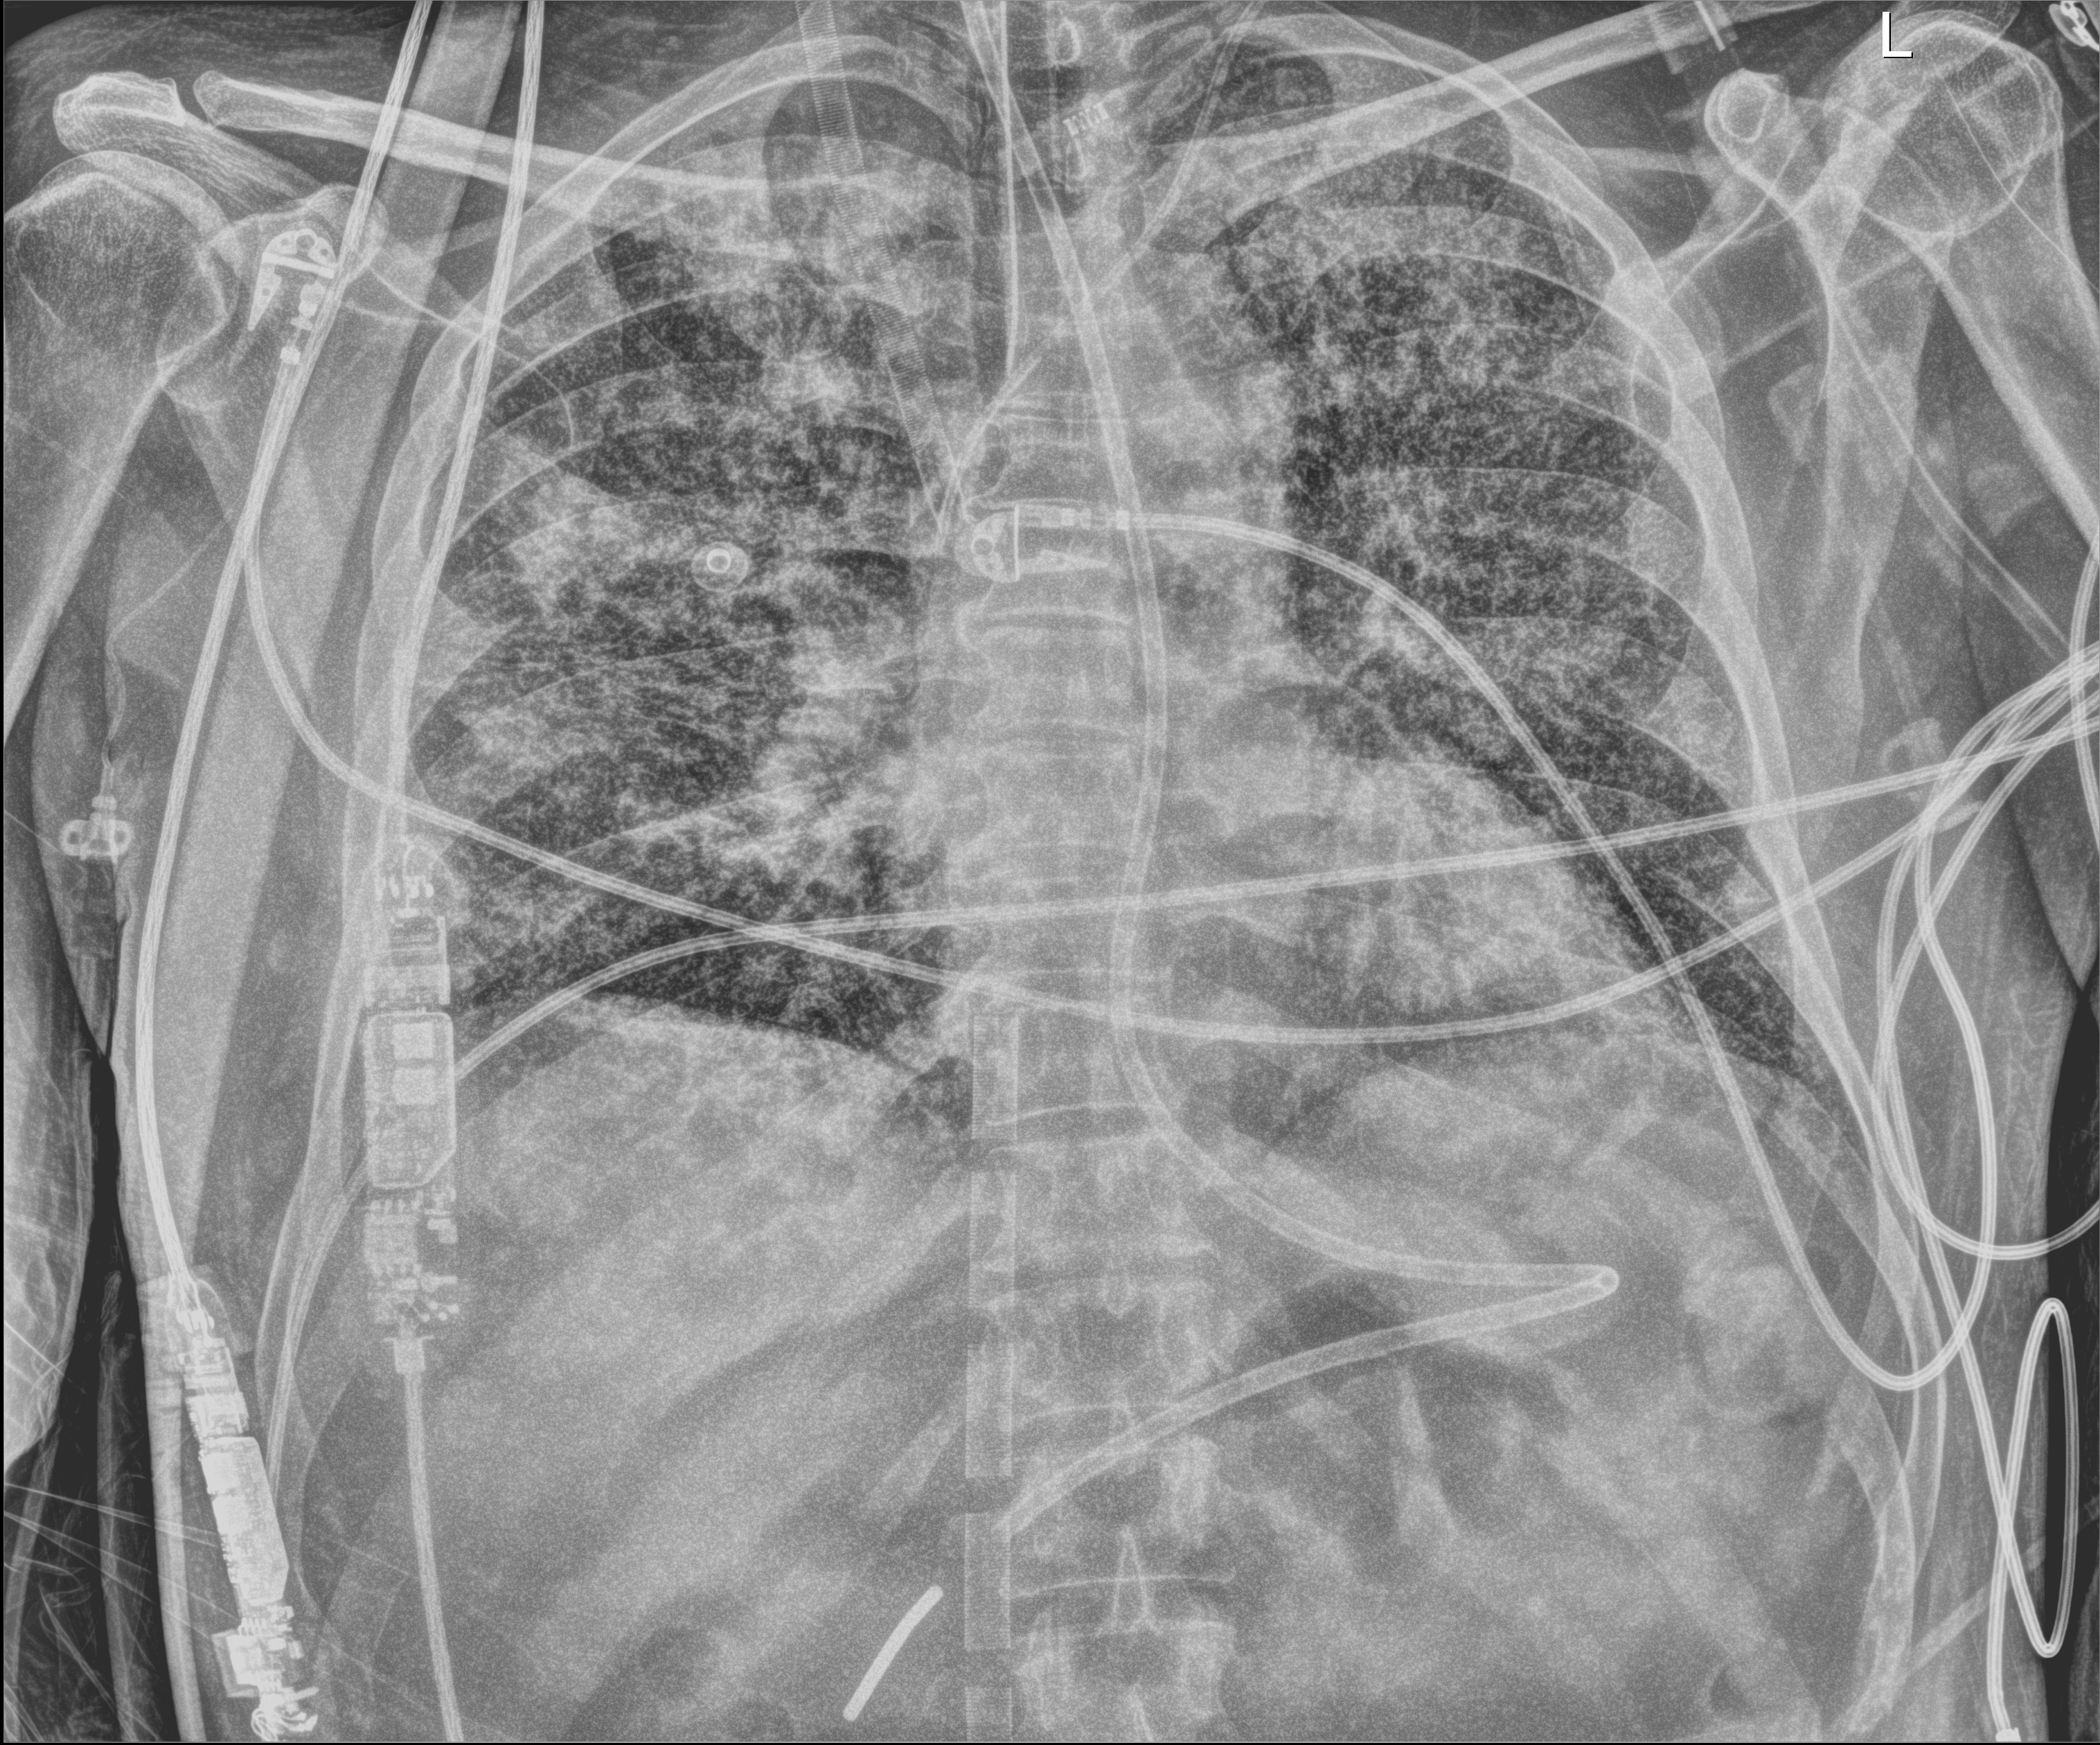
Chest radiograph (digital radiography), anteroposterior (AP) projection. Patient hospitalised with COVID-19; male, aged 18–59 years.
From the hospital-stay record, not from the radiograph (when in the stay this image was taken is not recorded): chronic kidney disease (admission record): no; admitted to intensive care during this hospital stay: yes; length of hospital stay: 42 days.